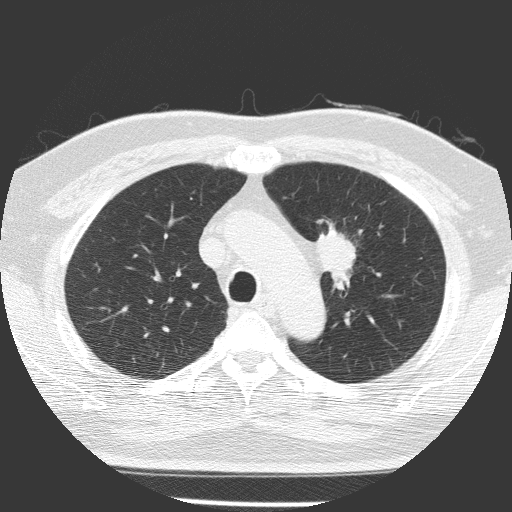
Low-dose screening chest CT, one axial slice; position 112 of 156 along the scan axis; reconstruction kernel FC51; lung window (W 1500 / L -600 HU); 2 mm slice thickness; 512 × 512 image matrix, field of view 309 × 309 mm.
Structures marked on this image (outlined manually by an expert reader):
- lesion 1 (tumor, upper lobe of left lung): bounding box (x1, y1, x2, y2) in pixels: (316, 224, 357, 287)